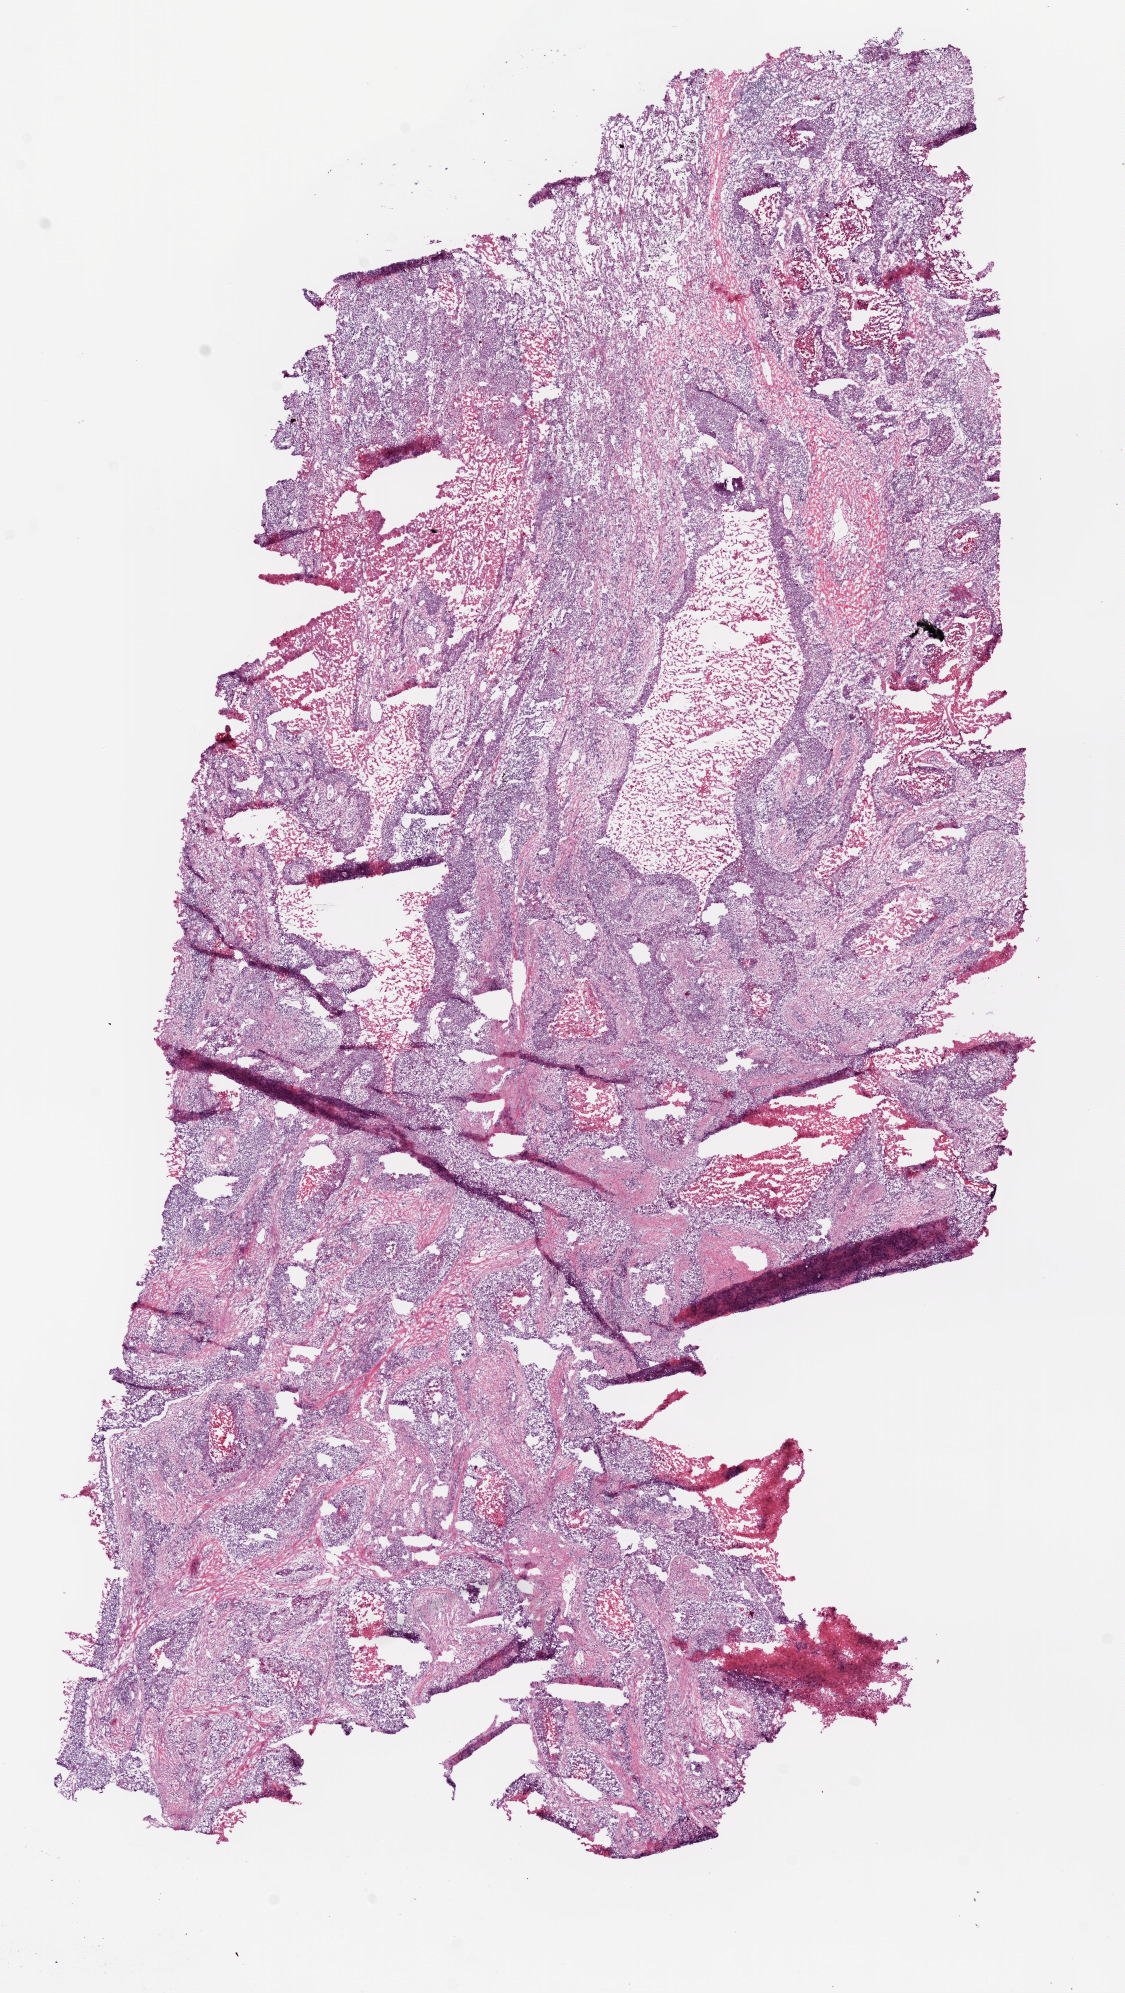
H&E-stained whole-slide image, shown as a low-resolution overview of the whole scanned area (about 9.0 x 16.0 mm). Frozen section. Sample: primary tumour, lung. Patient: male, age at initial diagnosis 76 years. Slide review estimates, as recorded: tumour cells 80%, tumour nuclei 85%, normal cells 0%, stromal cells 10%, necrosis 10%.
AJCC pathologic stage: IIIB. Laterality: right. Pathologic diagnosis: Squamous cell carcinoma, NOS (upper lobe, lung).